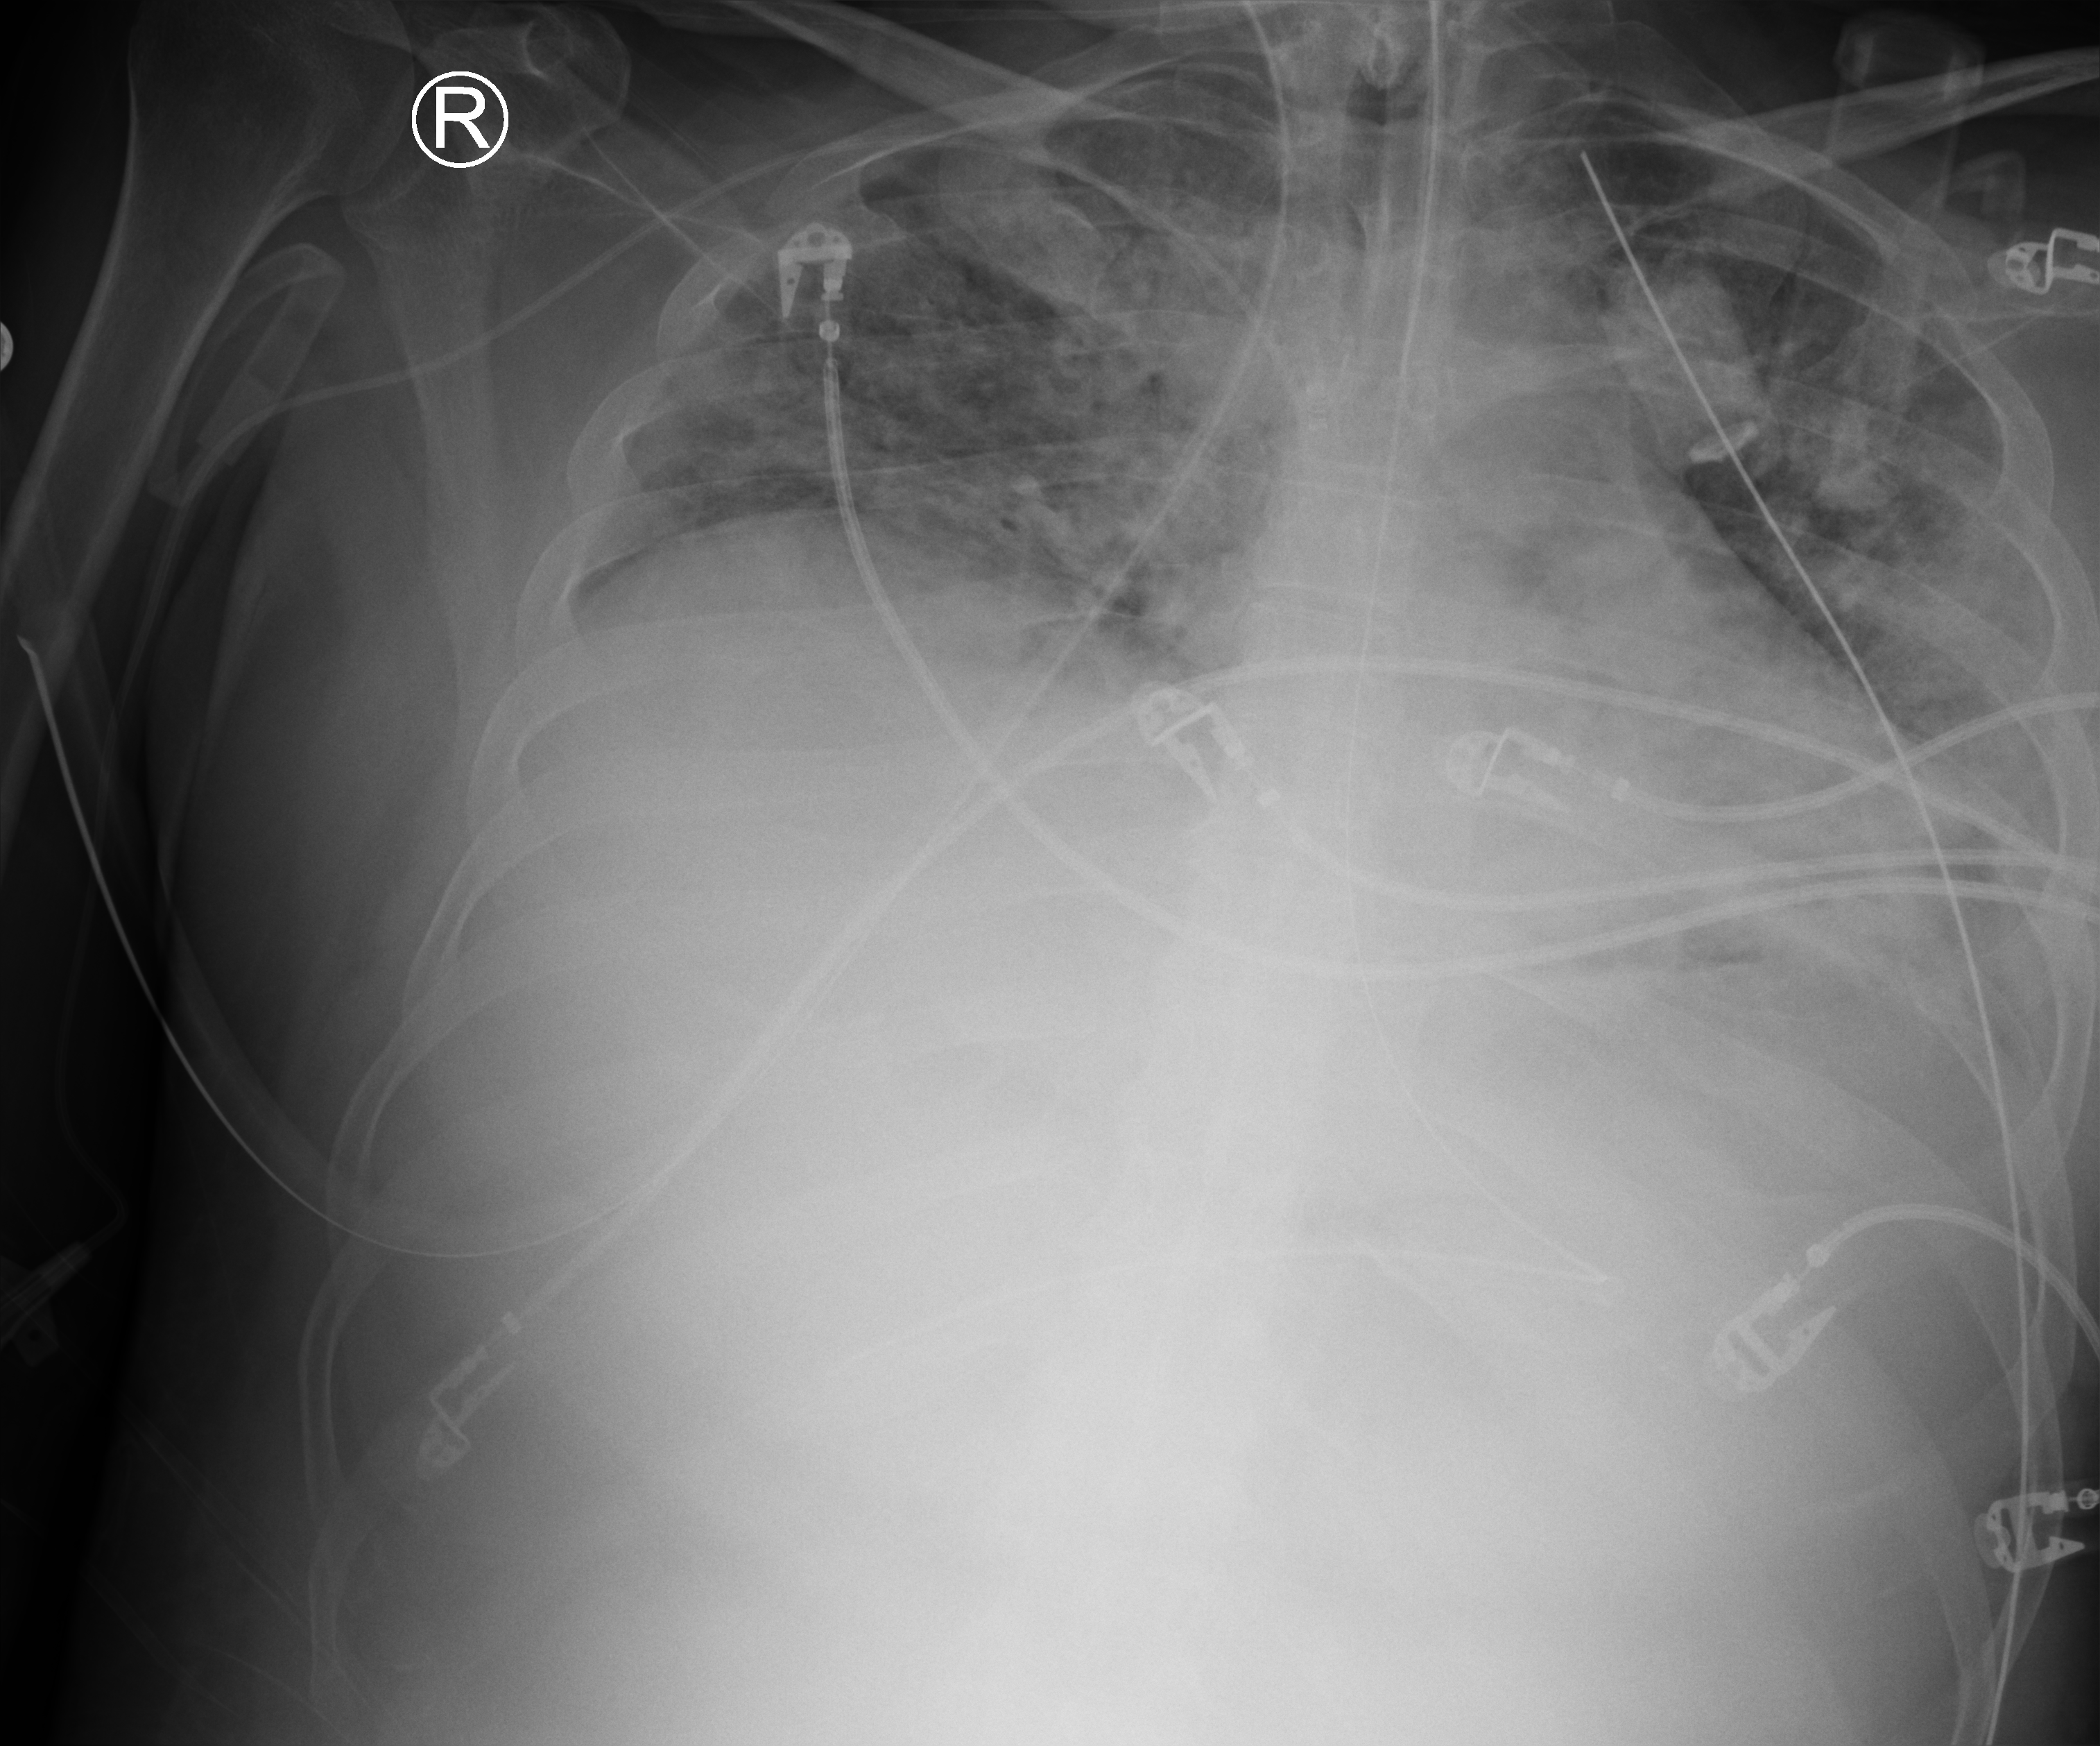
Portable chest radiograph; anteroposterior (AP) projection. Male patient hospitalised with COVID-19, age 18–59 years.
Hospital-stay facts (about this admission, not read from this image; timing relative to this image not recorded): mechanically ventilated during this hospital stay: yes; hypertension (admission record): no; COPD (admission record): no.